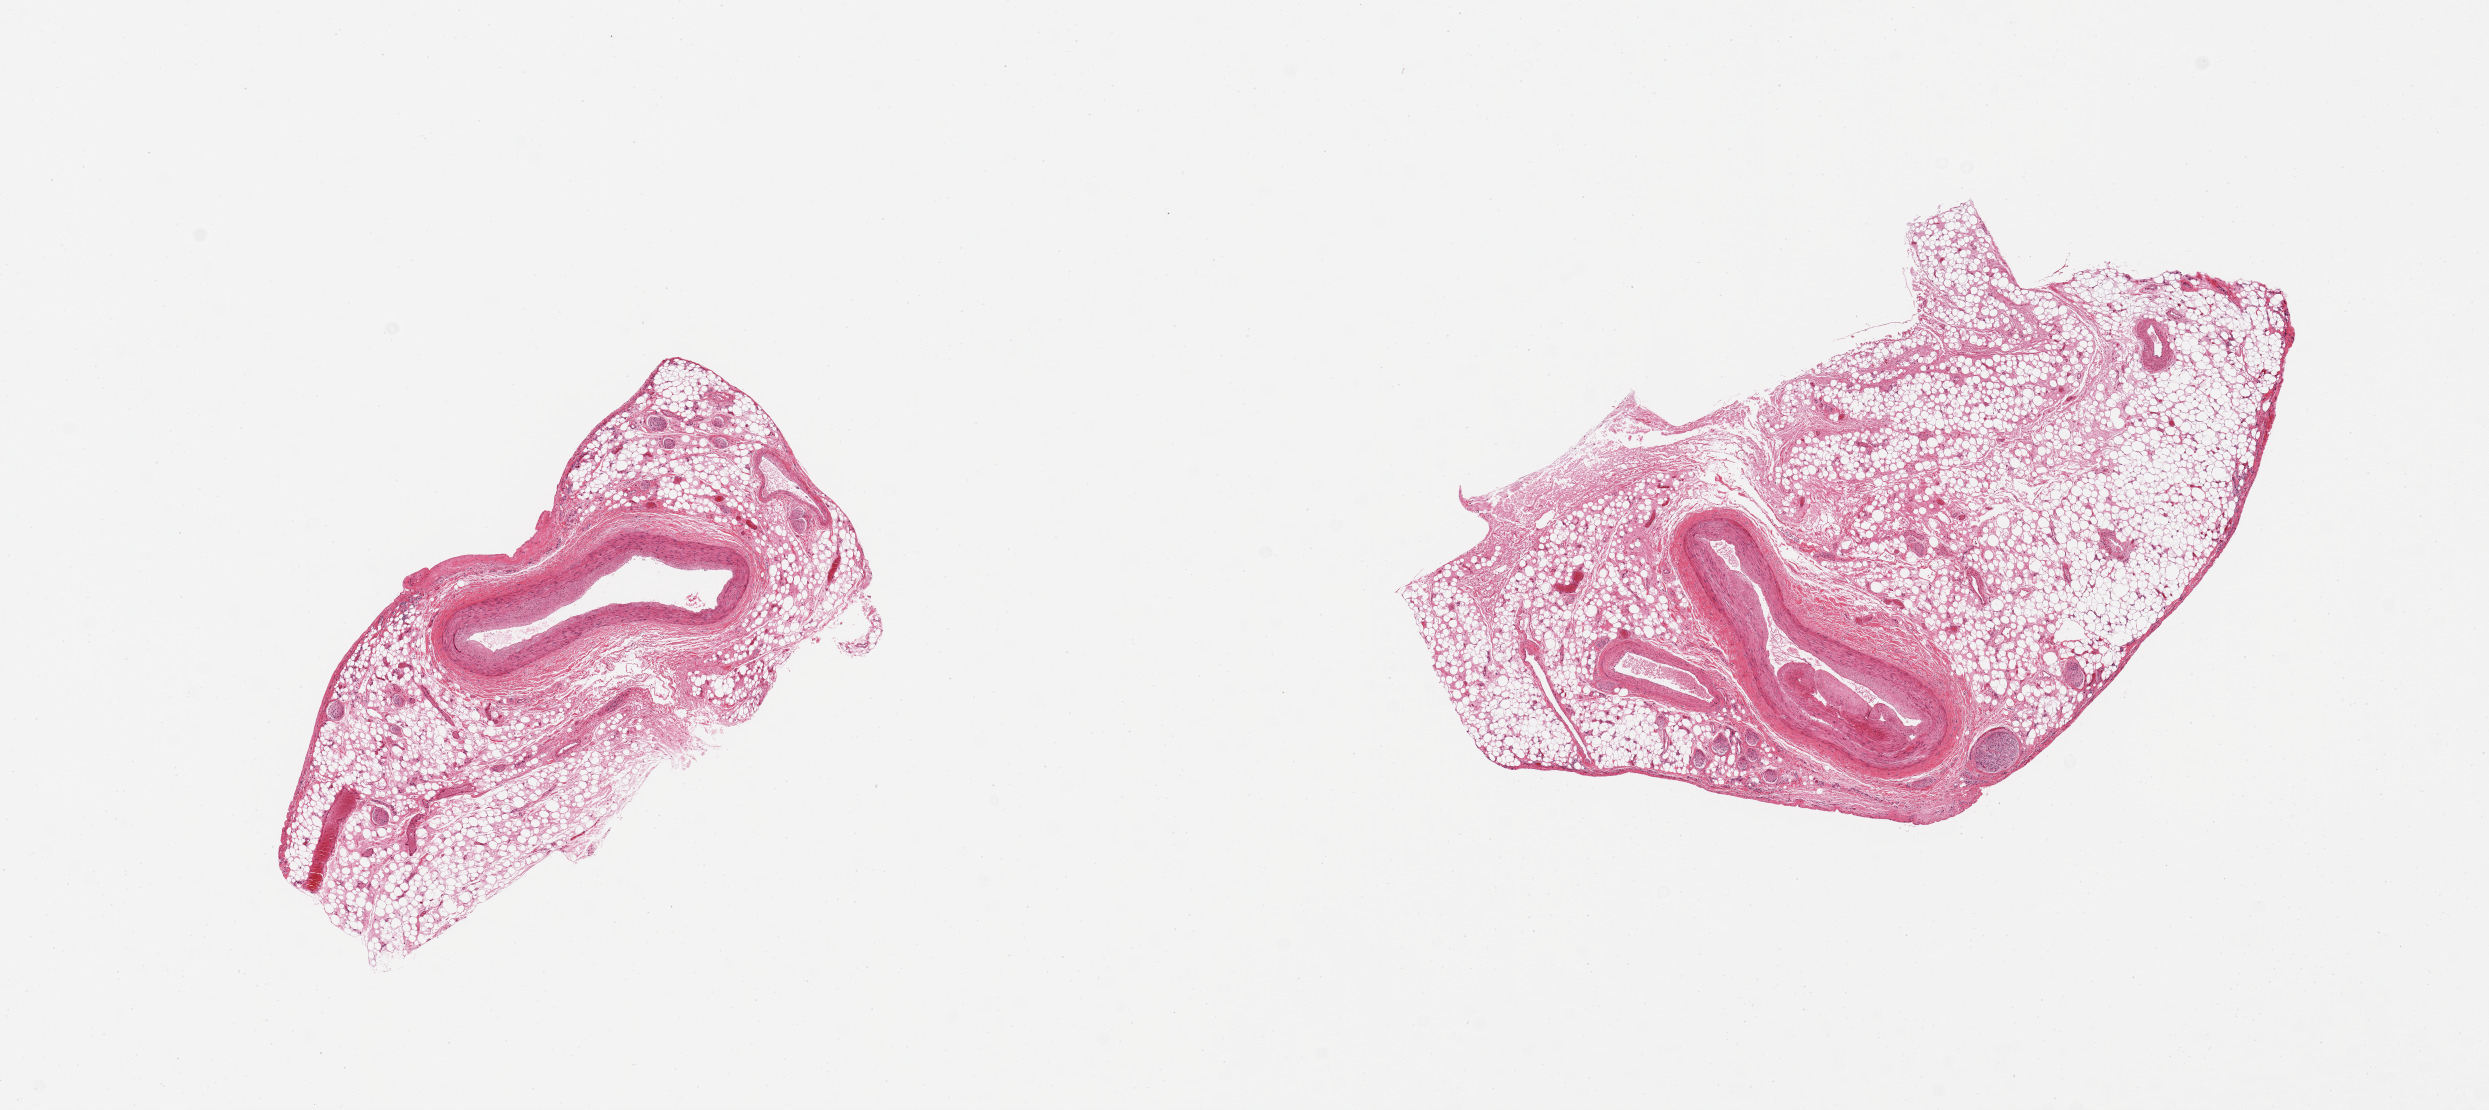
Digitized haematoxylin and eosin-stained section, shown as a low-resolution overview of the whole scanned area (about 19.7 x 8.8 mm, slide scanned at 20x); PAXgene-fixed paraffin-embedded (PFPE) section; section of coronary artery (target tissue); donor tissue sample. Female donor.
Review note (as recorded): 2 pieces, up to 4mm aderent fat/nerve/vessel.